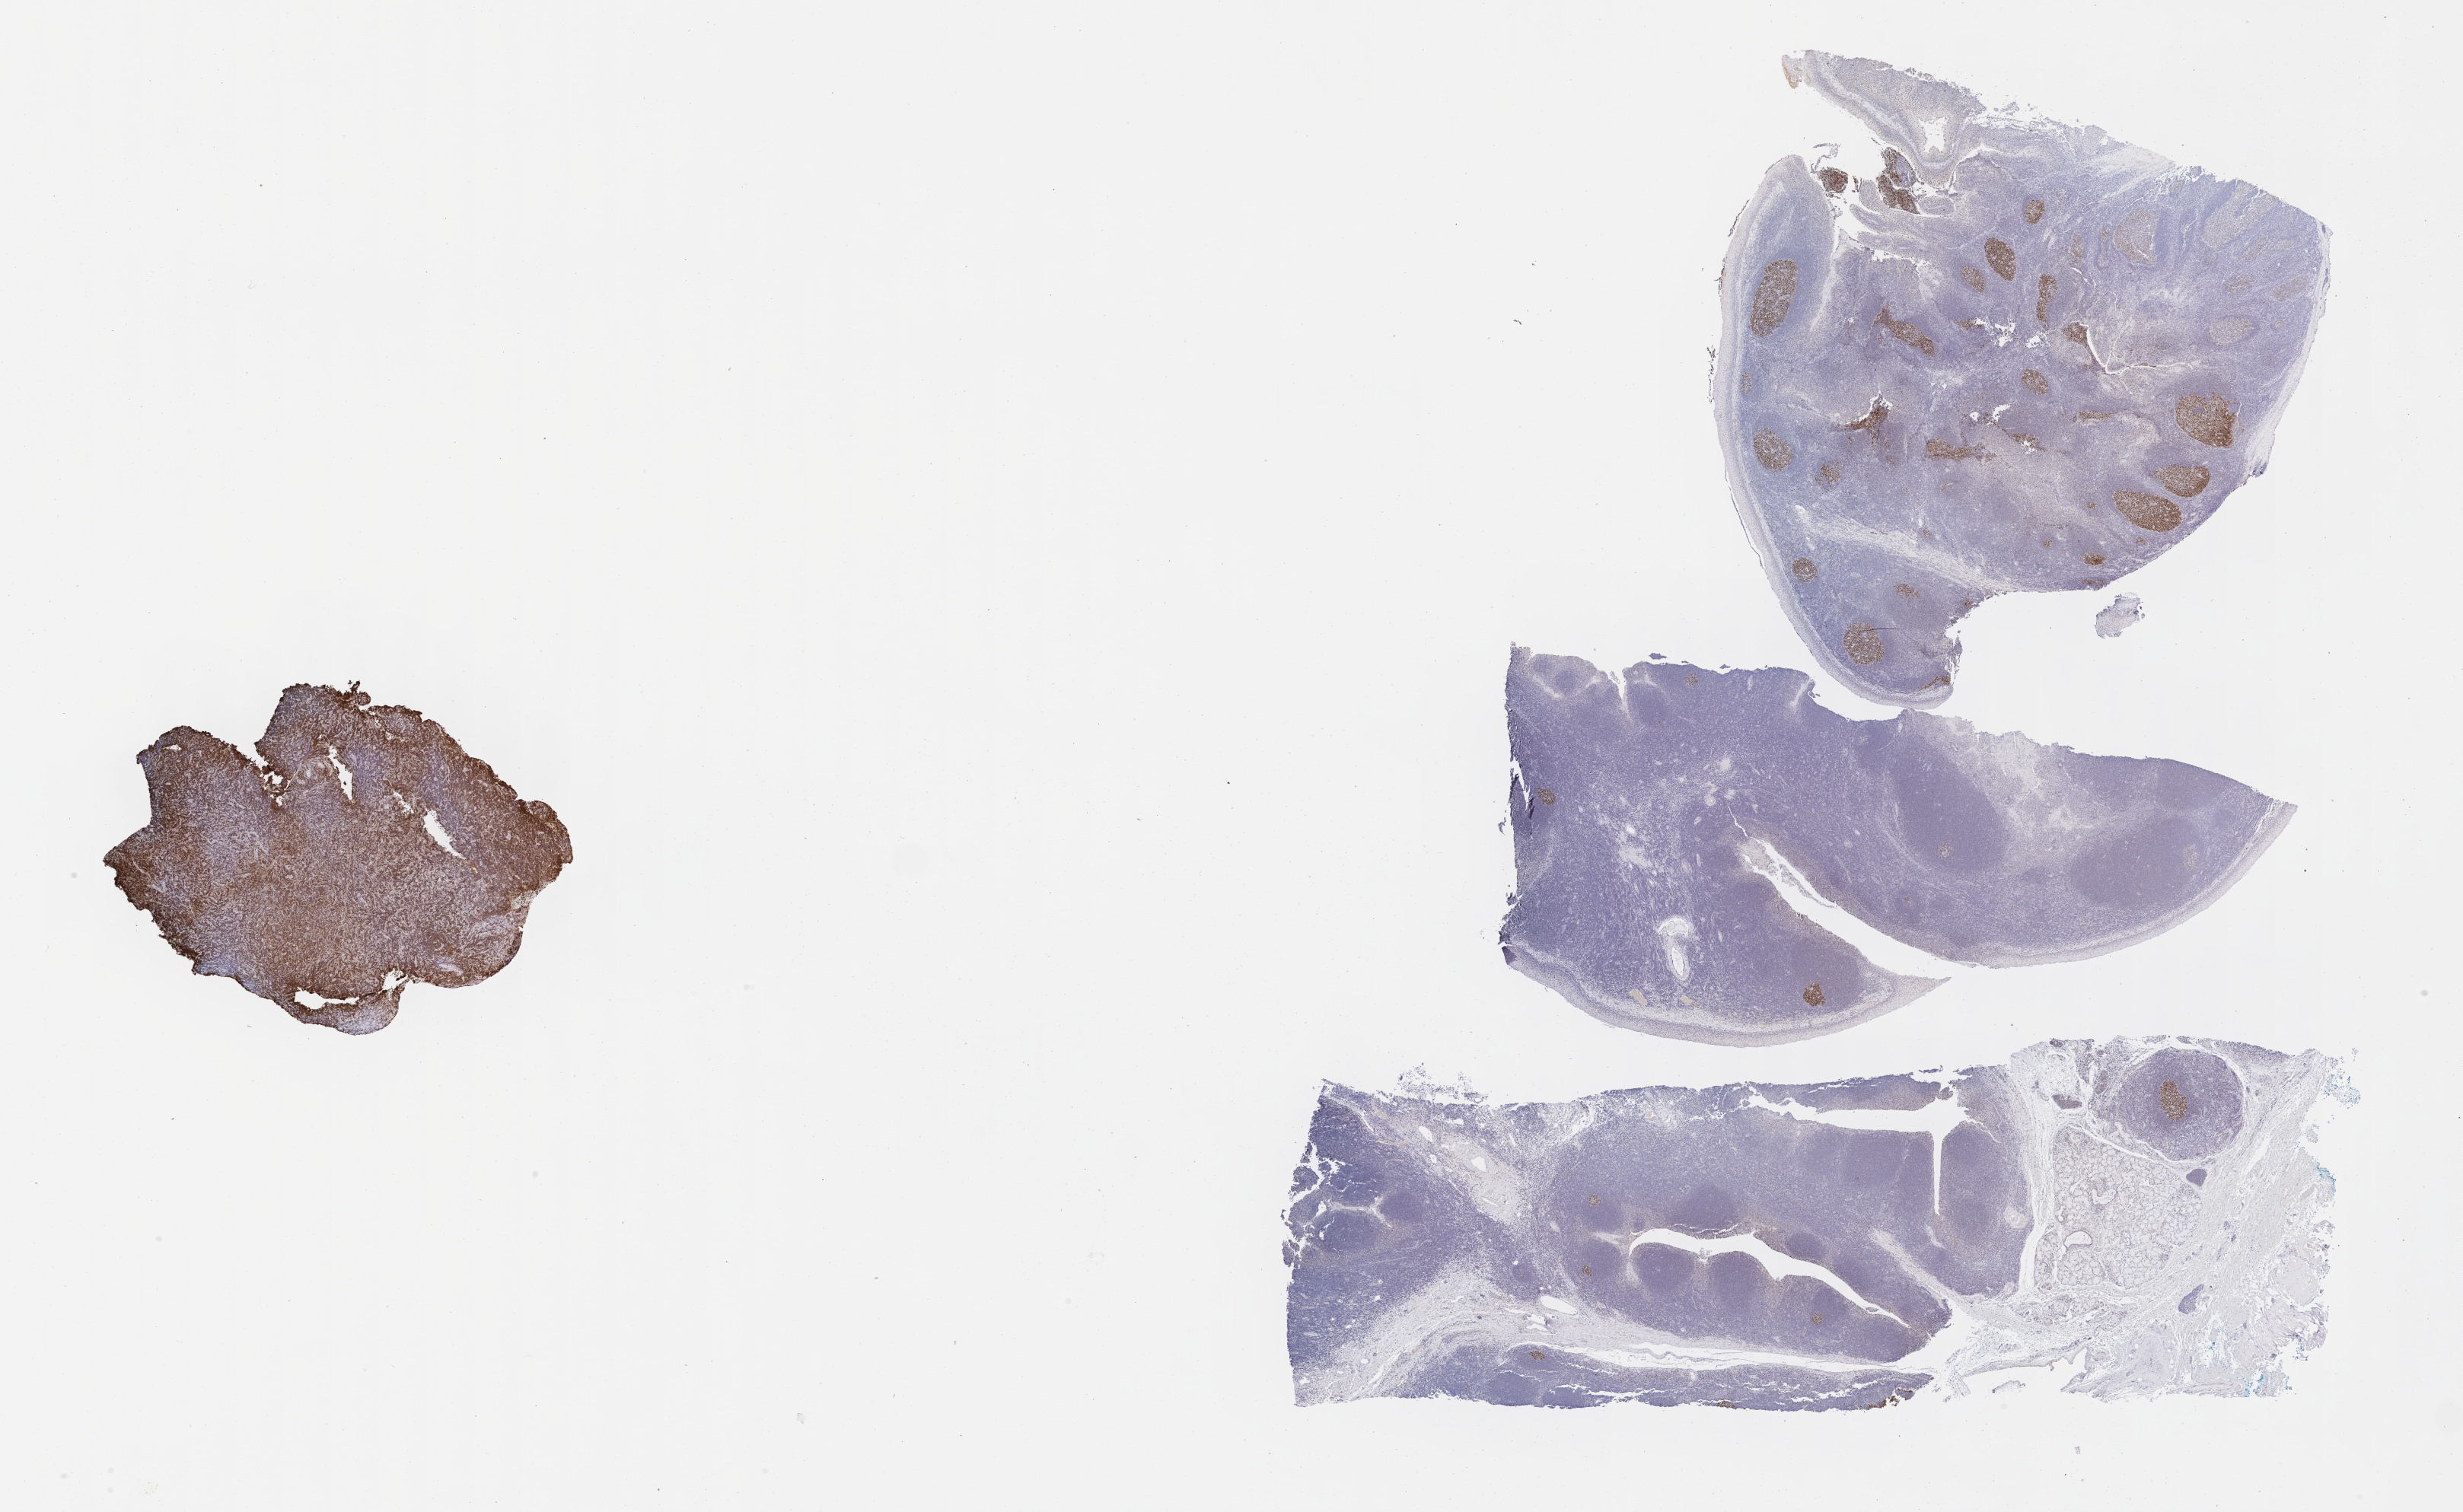
Immunohistochemistry (IHC) whole-slide image stained for BCL6 — whole scanned area (about 26.2 x 16.1 mm) shown as a low-resolution overview. Tumor tissue. Anatomic site: mandible. Male patient; age at initial diagnosis 8 years.
Histologic diagnosis: Burkitt lymphoma, NOS.